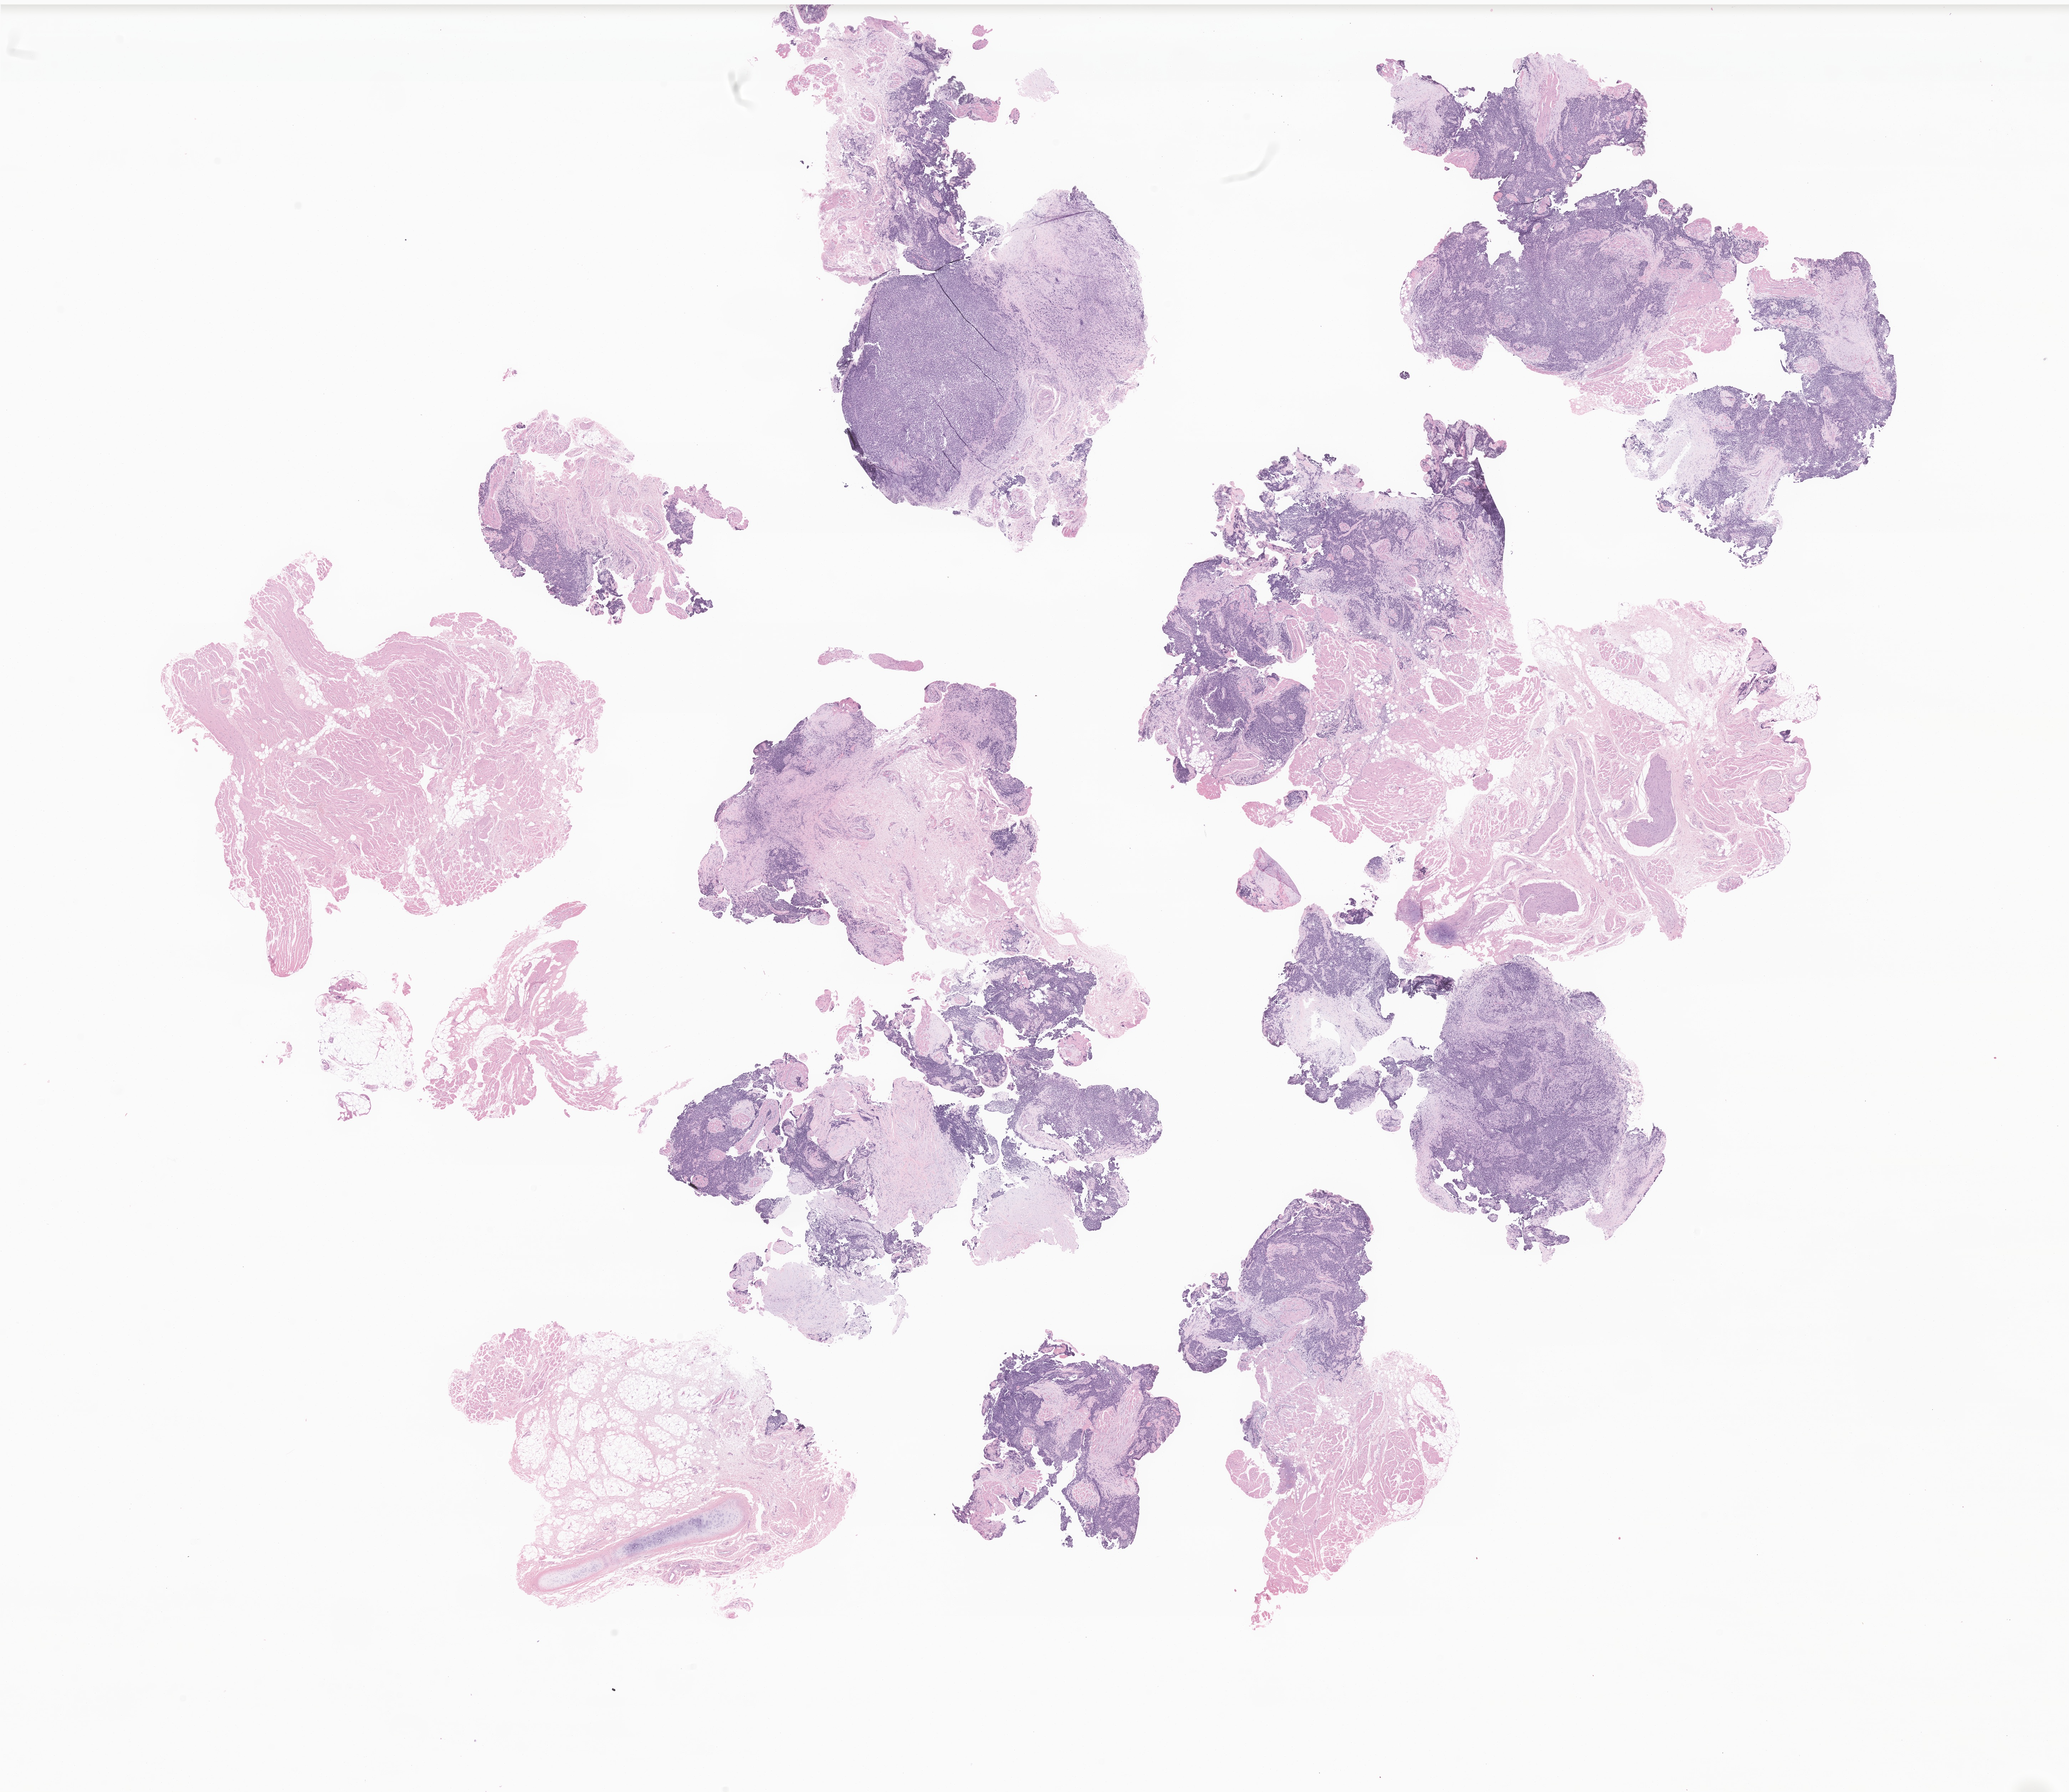
Haematoxylin and eosin whole-slide image of tumor tissue from the soft tissues of head and neck, shown as a low-resolution overview of the whole scanned area (about 24.5 x 21.2 mm); formalin-fixed paraffin-embedded section. Male patient, age 88 months (7 years 4 months).
Recorded diagnosis: Embryonal rhabdomyosarcoma, NOS.